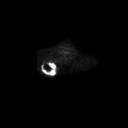
FDG PET of an extremity soft-tissue mass (from a PET/CT study), one axial slice. Position 217 of 267 along the scan axis. 128 × 128 image matrix, field of view 700 × 700 mm. Male patient, age 61 years. Case-level facts recorded for this patient, not image findings: histological type: pleiomorphic spindle cell undifferentiated; grade: high; site of the primary tumour: right parascapusular.
Outlined on this slice (expert contour drawn on MRI and transferred to this co-registered scan by the dataset authors):
- gross tumour volume including surrounding oedema: bounding box [x1, y1, x2, y2] px = [41, 61, 59, 75]
- gross tumour volume (mass): [42, 63, 54, 74]